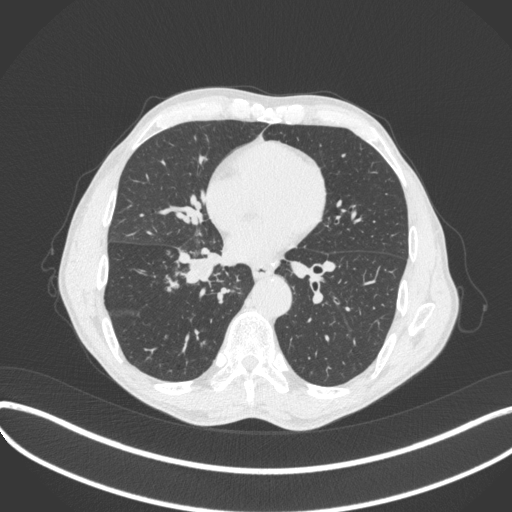
Chest CT, one axial slice; 120 kVp; lung window (W 1500 / L -600 HU); 1 mm slice thickness; 512 × 512 image matrix, field of view 400 × 400 mm. Patient: male, 65 years. From the clinical record (not read from this slice): clinical TNM (as recorded): T2a N0 M0; histopathological grade: G2.
Annotated regions visible in this slice (rectangle marked by the reading radiologist):
- lung tumour (recorded histology: squamous cell carcinoma): bounding box [x1, y1, x2, y2] px = [173, 246, 232, 293]